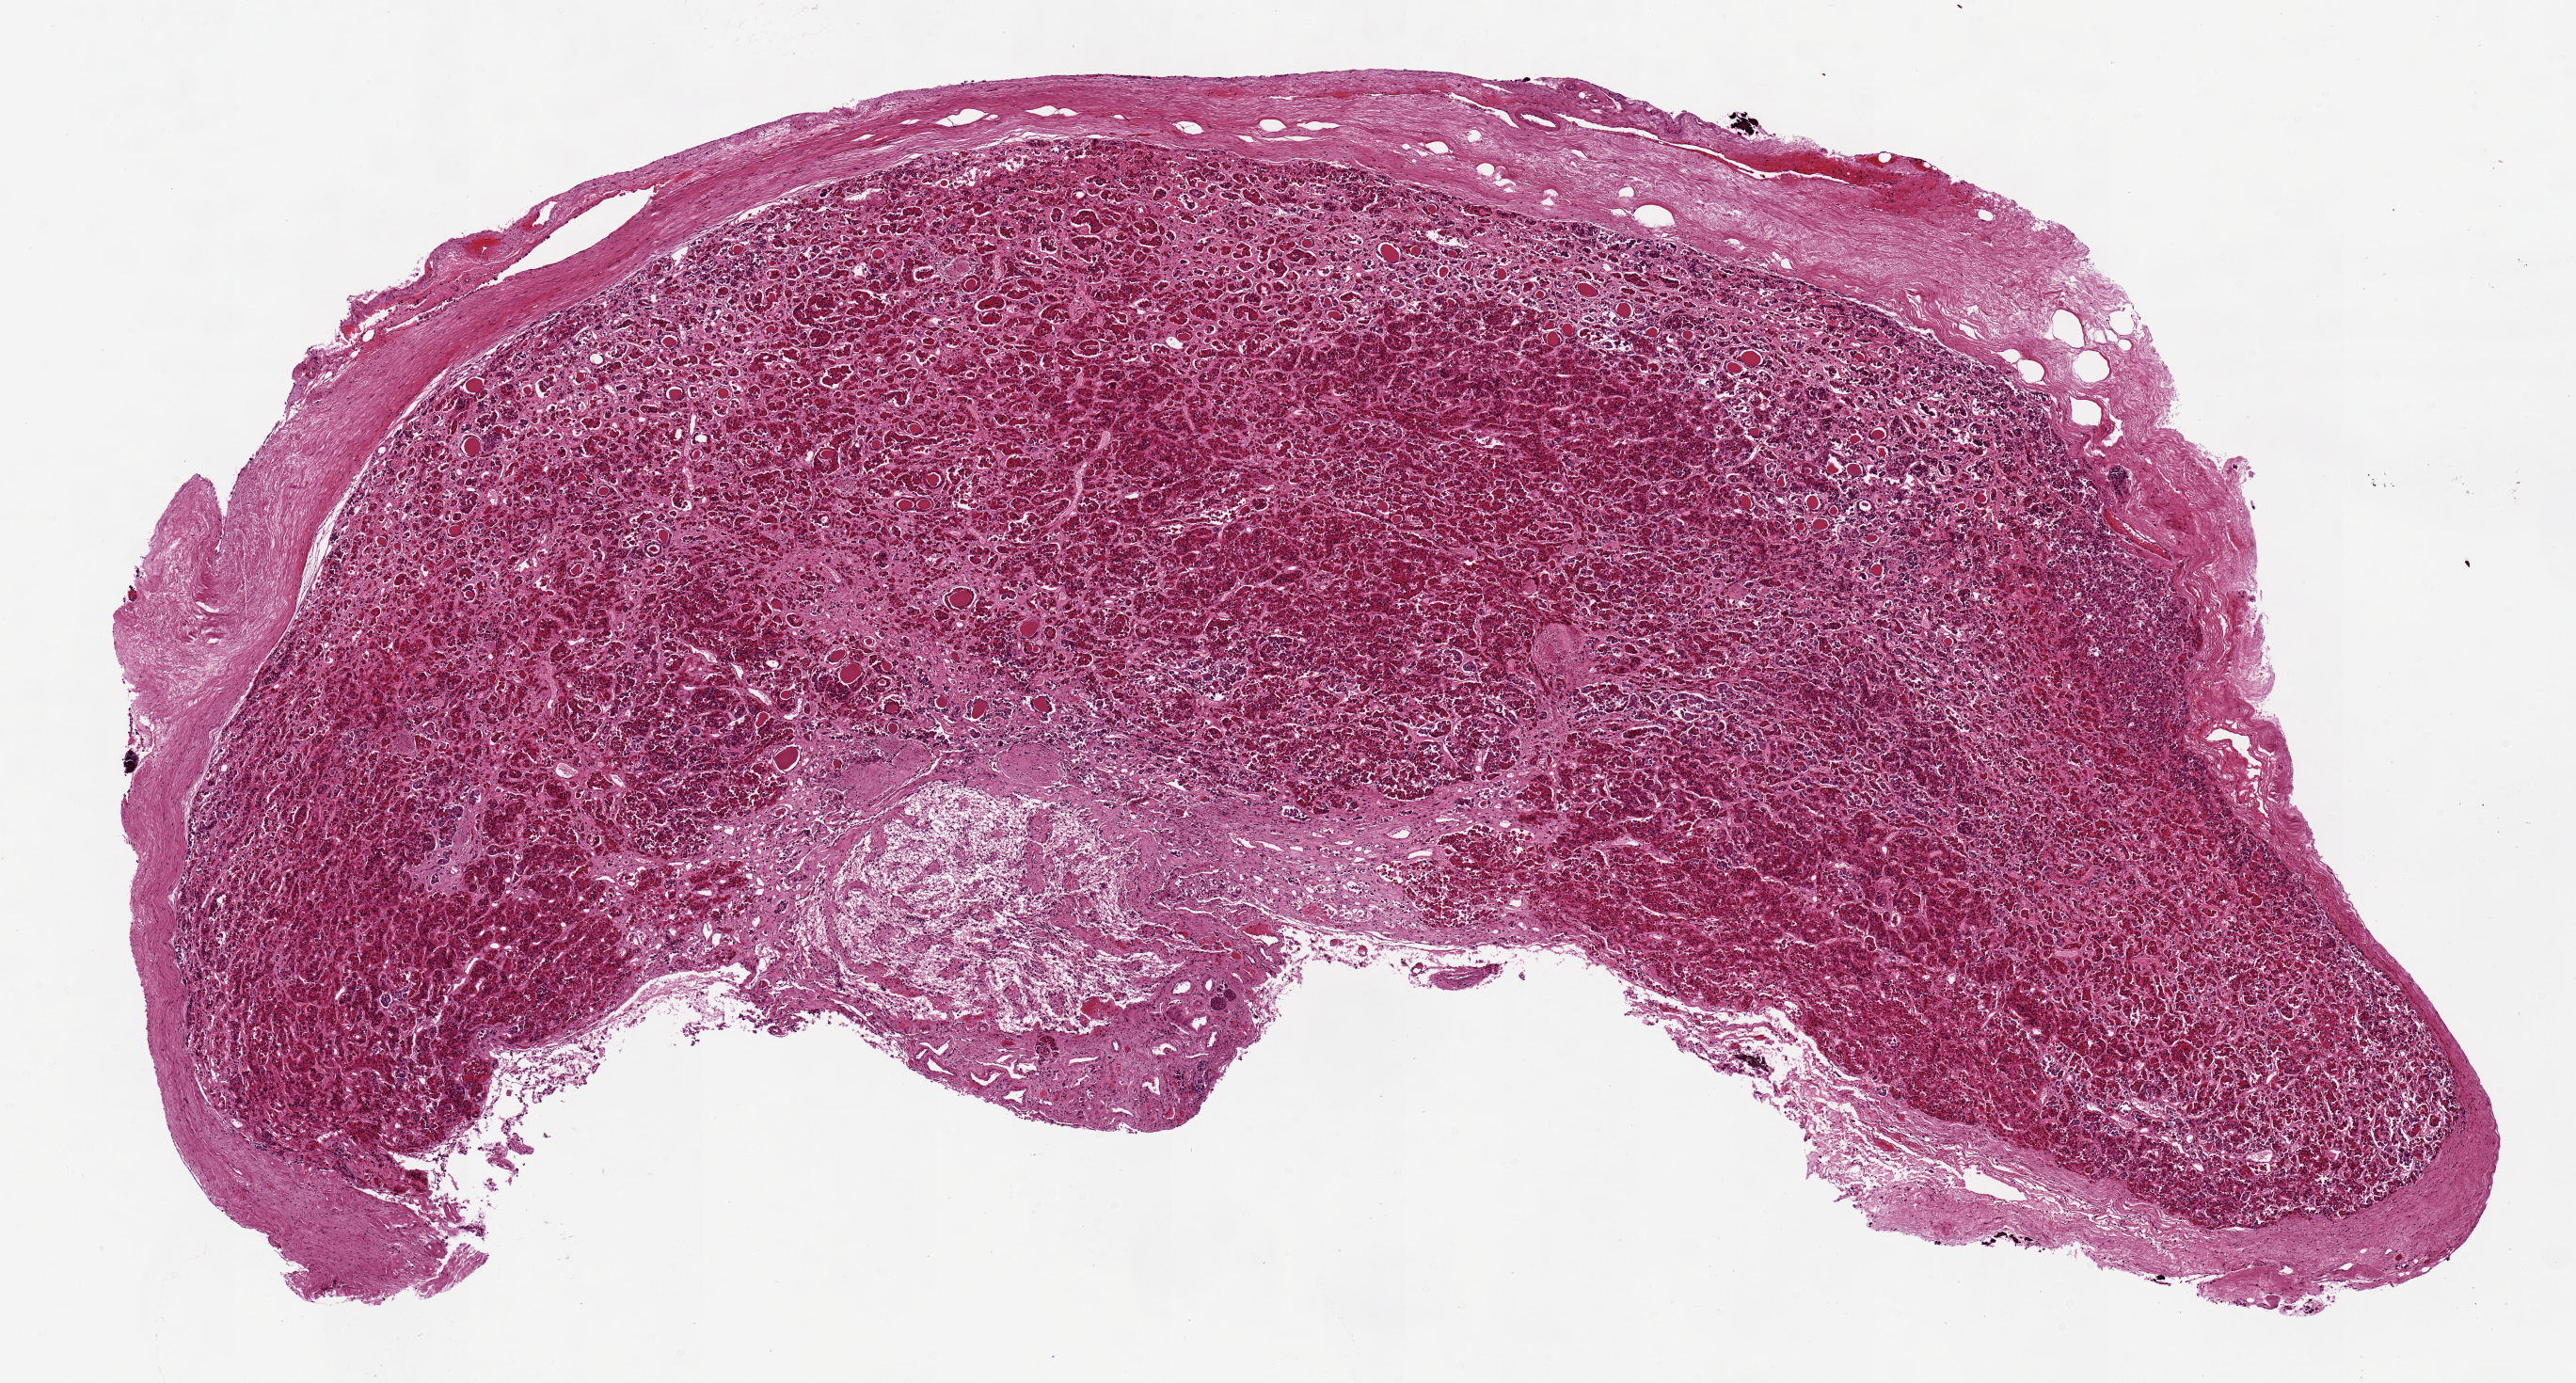
Digitized hematoxylin and eosin (H&E)-stained section, a low-resolution overview of the entire scanned area, about 10.8 x 5.8 mm, PAXgene-fixed paraffin-embedded (PFPE) section, target tissue: pituitary, donor tissue sample. Donor sex: female.
Review note (as recorded): Mild autolysis (???score 1???).